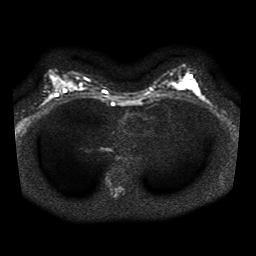
Breast MRI, one axial slice; position 21 of 41 along the scan axis; diffusion-weighted series; image 2 of 4 stored at this slice position (different b-values; order by instance number); 1.5 T; 5 mm slice thickness; 256 × 256 image matrix. Female patient.
Annotated regions visible in this slice (expert manual segmentation):
- tumour on diffusion-weighted imaging: bounding box (x1, y1, x2, y2) in pixels: (186, 78, 196, 90)